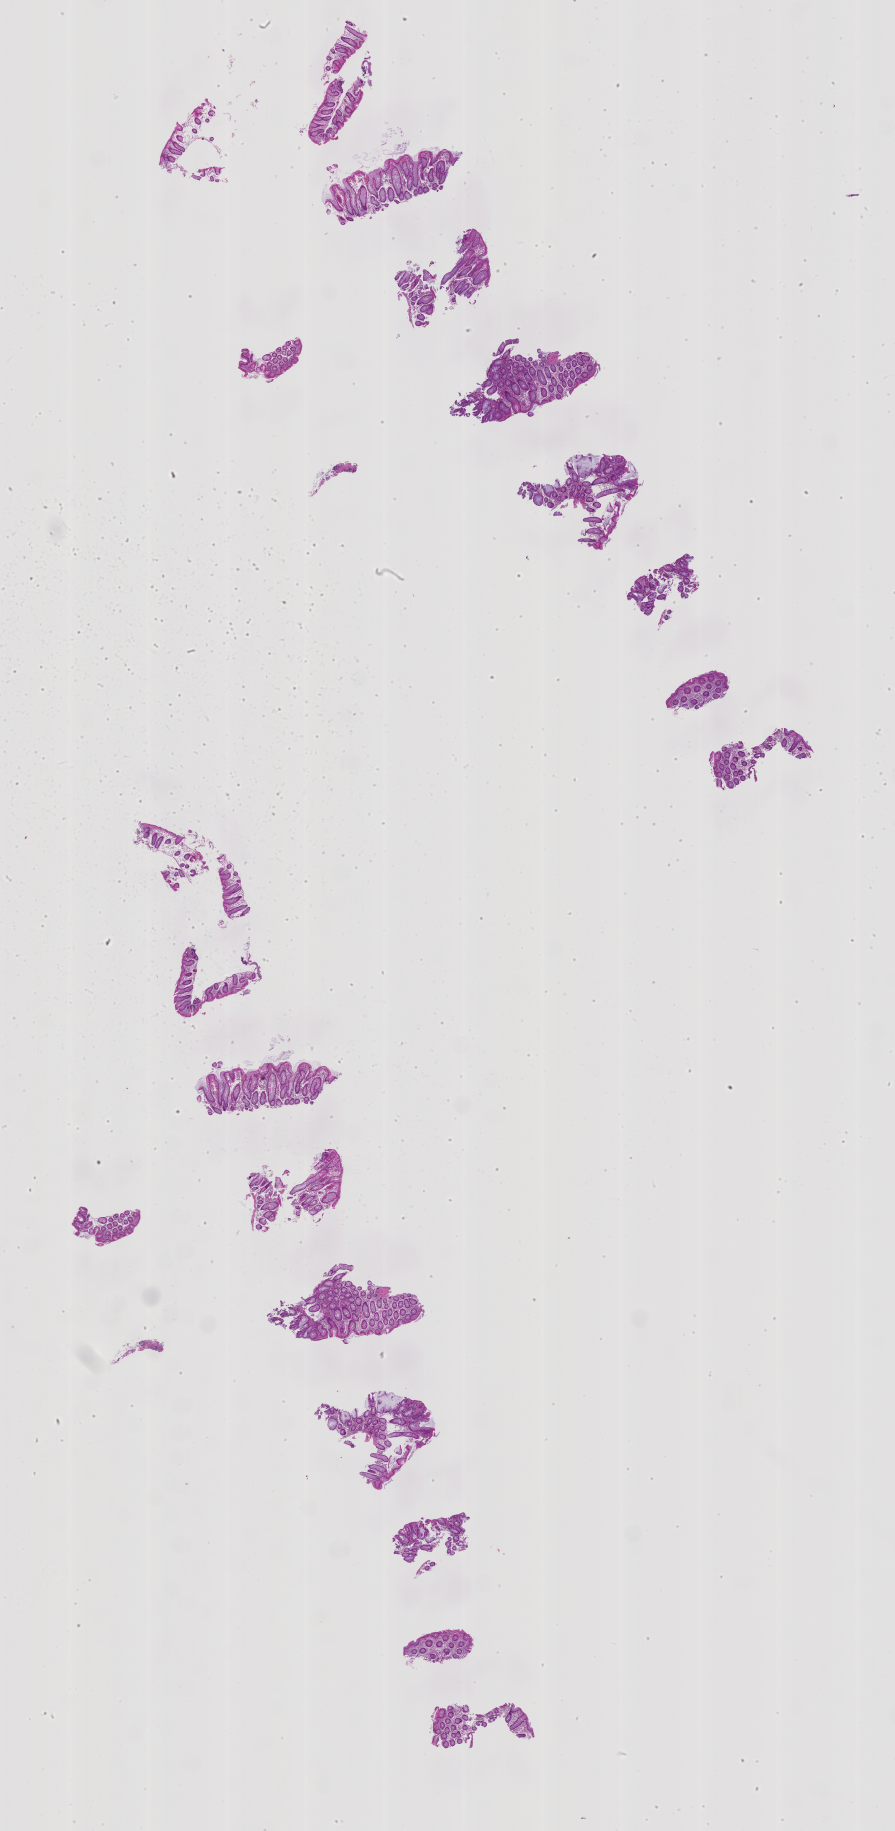
H&E whole-slide image of a colon biopsy — a low-resolution overview of the entire scanned area, about 14.3 x 29.3 mm, formalin-fixed paraffin-embedded section, site: ascending colon. Patient: male.
Lesion category (as recorded): premalignant.